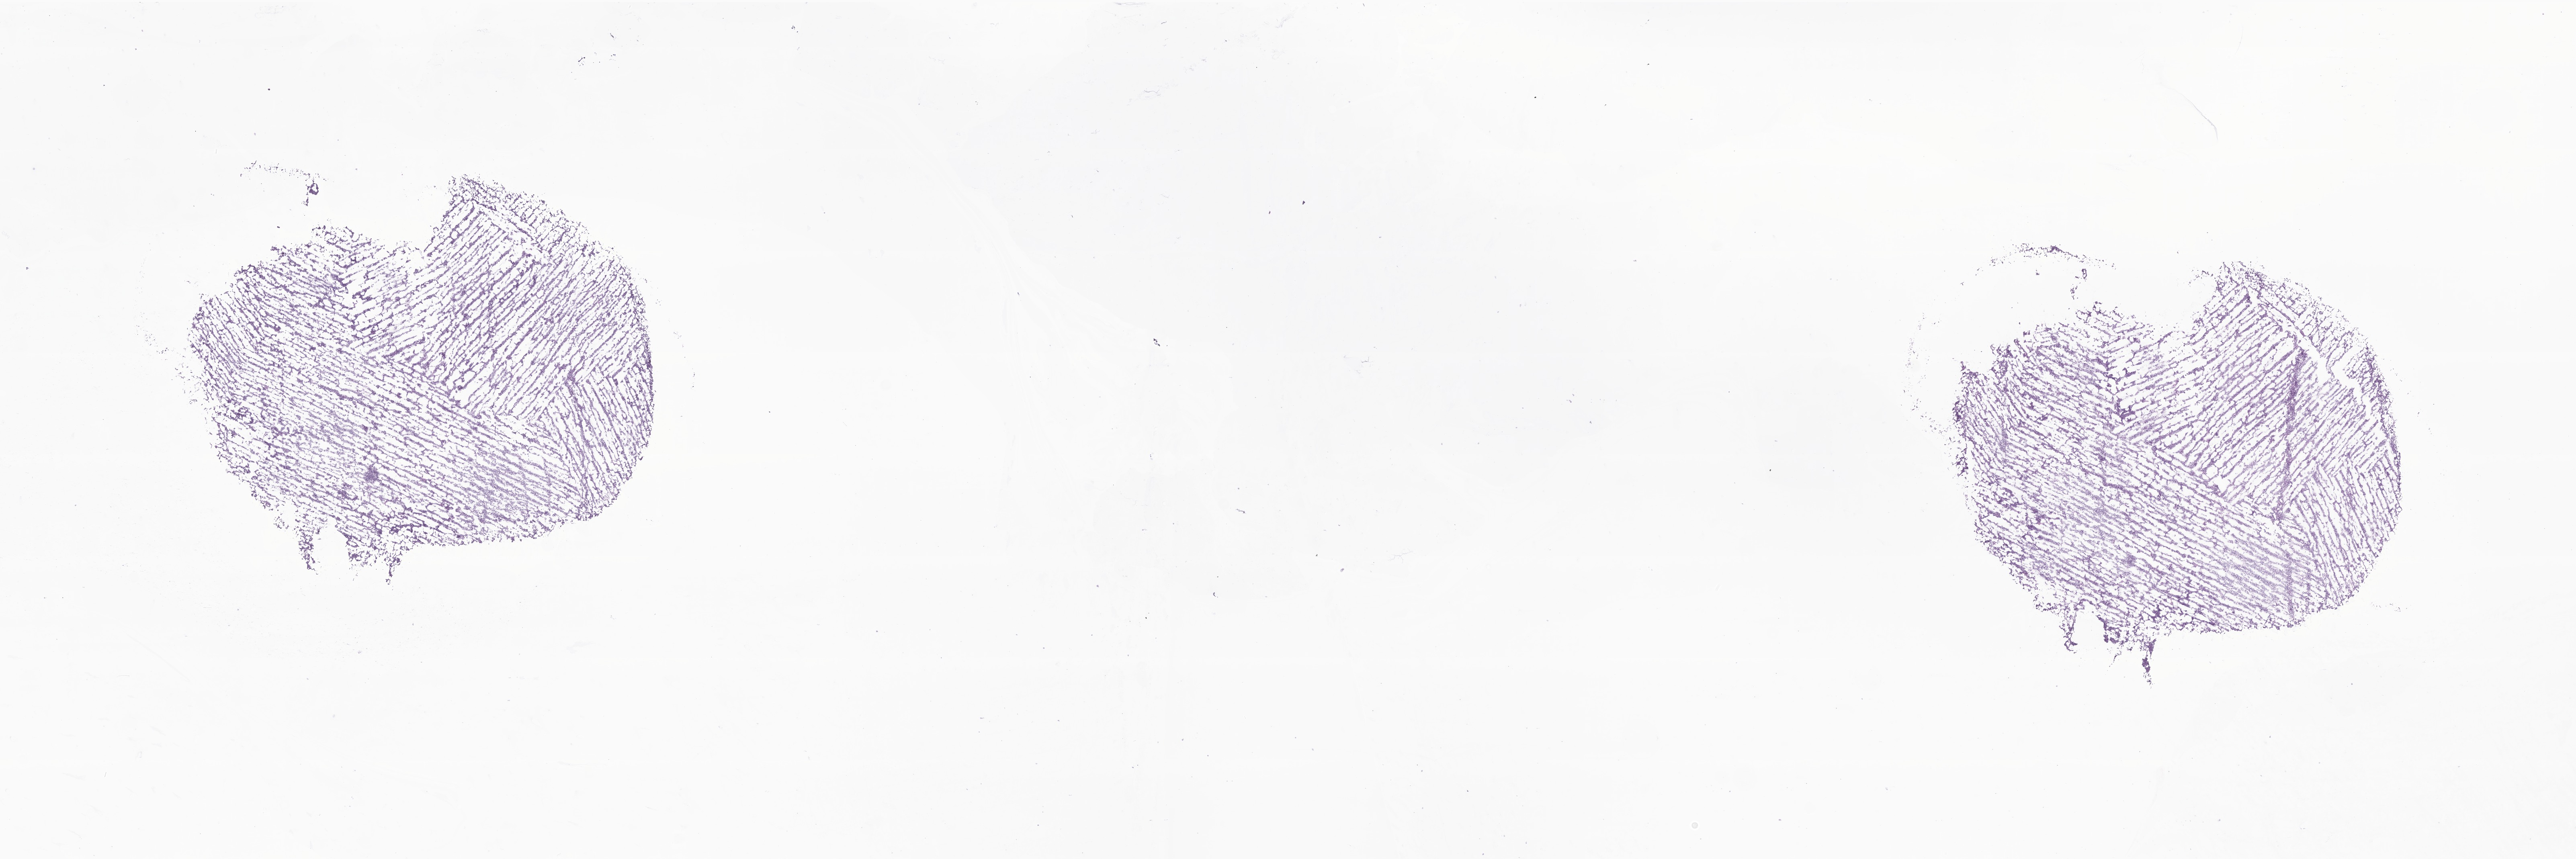
Whole-slide image, H&E stain of tumor tissue from the brain stem, low-resolution overview of the scanned area, about 27.0 x 9.0 mm; frozen section (OCT-embedded). Male patient, age 607 days.
- diagnosis: Neoplasm, malignant